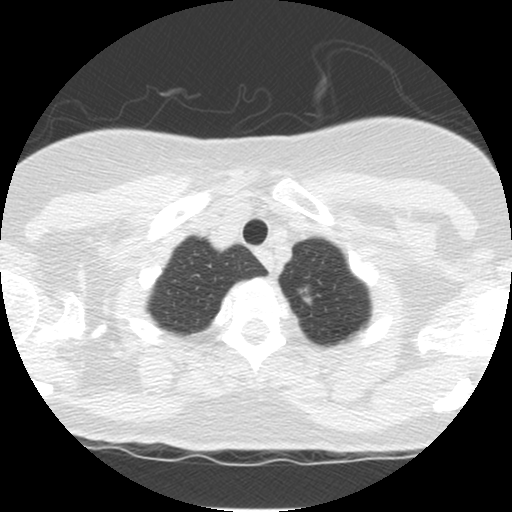
Low-dose screening chest CT, one axial slice; slice 112 of 120 in the series (ordered by position); reconstruction kernel STANDARD; 120 kVp; lung window (W 1500 / L -600 HU); 2.5 mm slice thickness; 512 × 512 image matrix, field of view 300 × 300 mm.
Annotated regions visible in this slice (outlined manually by an expert reader):
- lesion 1 (tumor, upper lobe of left lung): box from (x=299, y=285) to (x=312, y=305) px